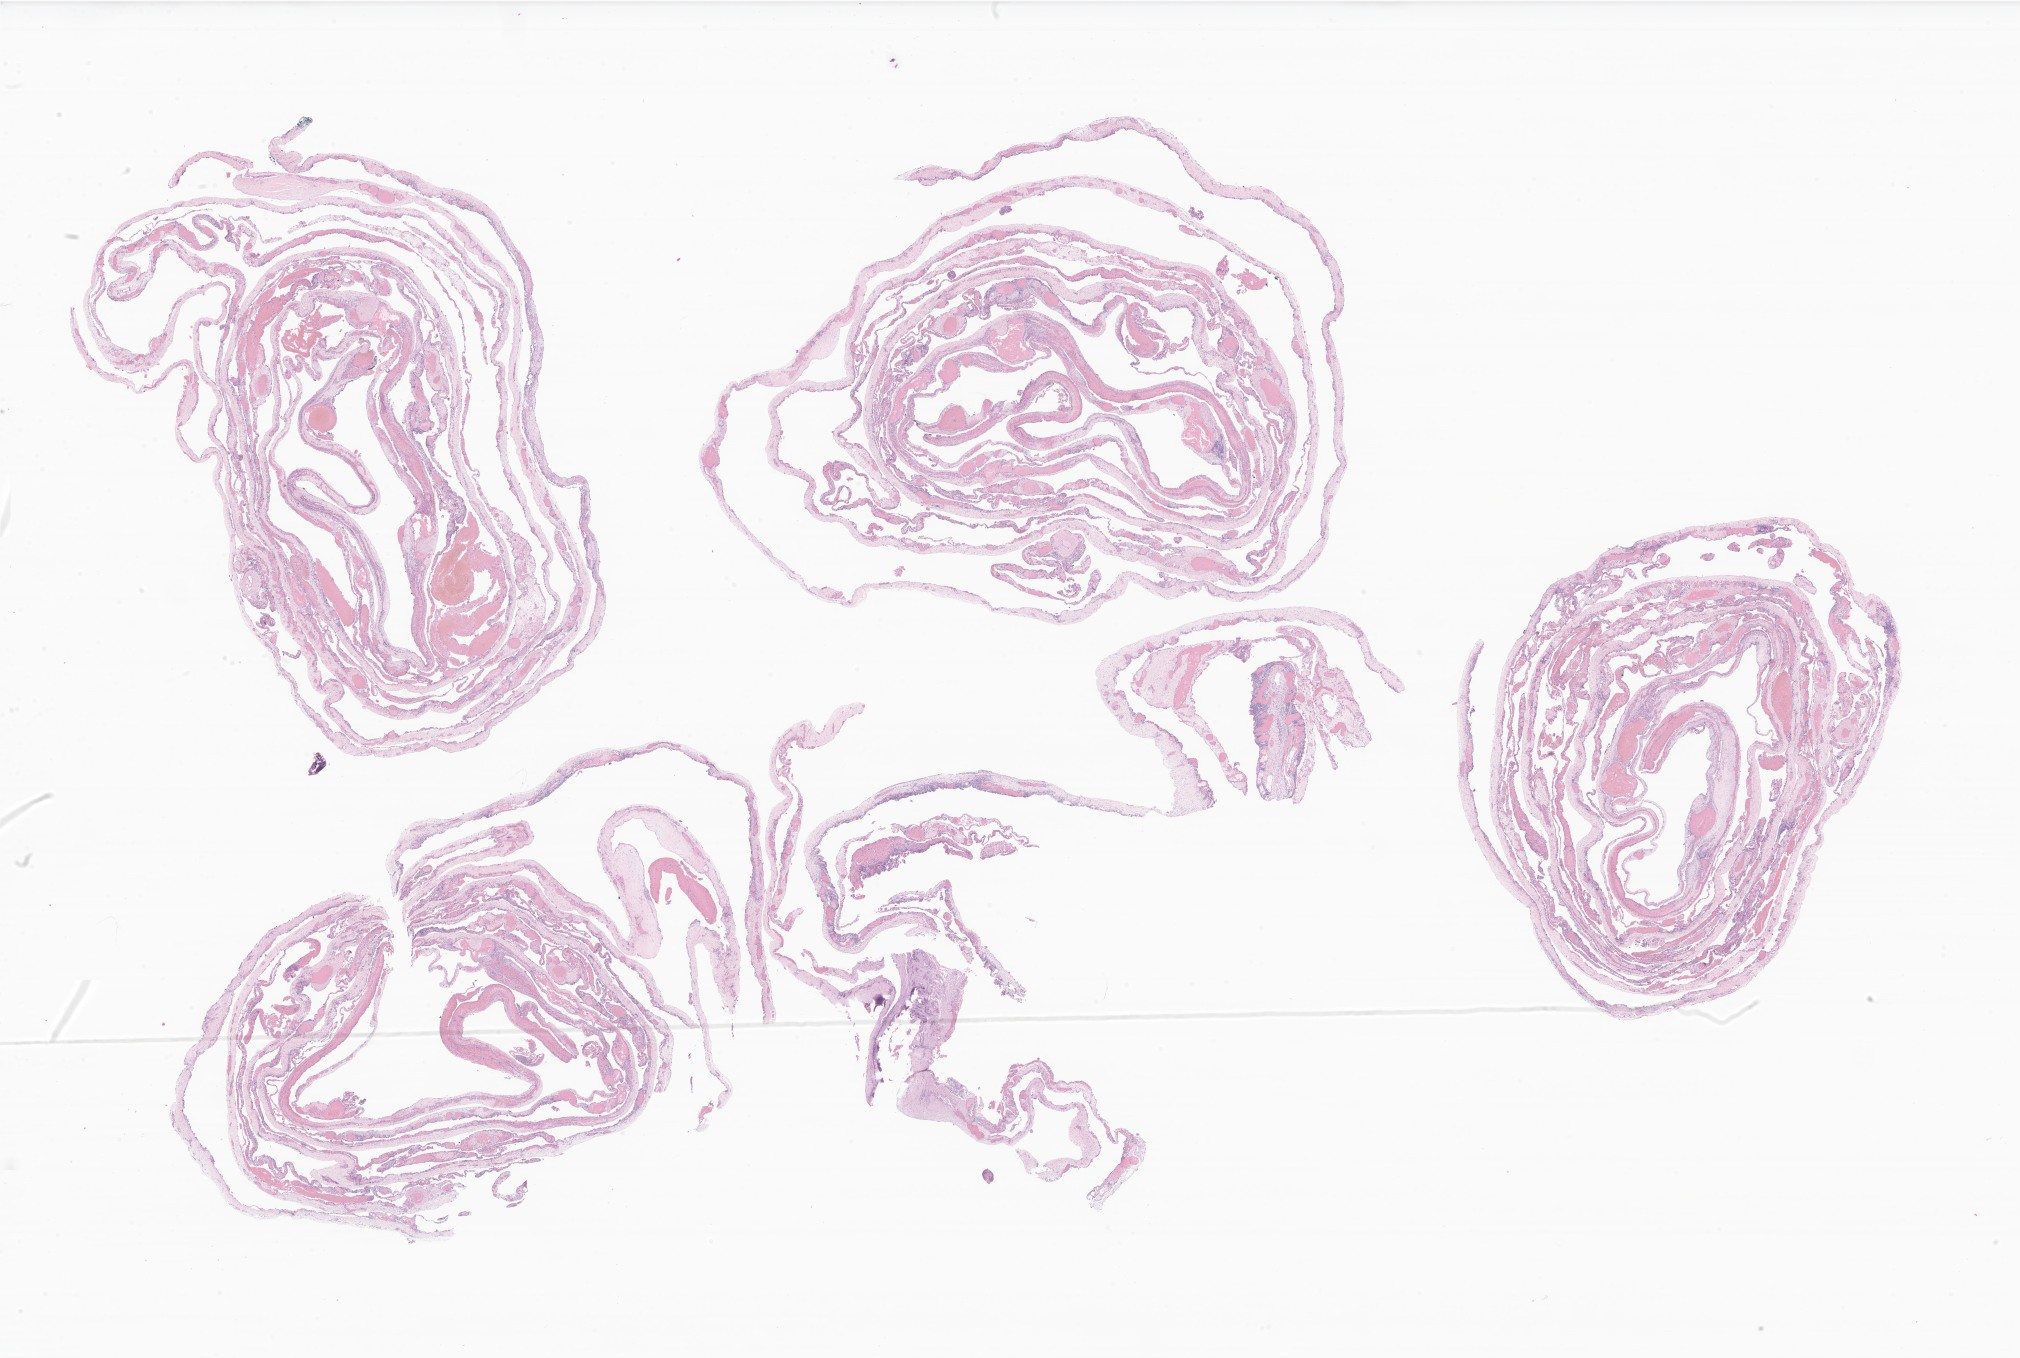
Digitized H&E-stained section of tumor tissue from the lung, low-resolution overview of the scanned area, about 34.1 x 22.9 mm, formalin-fixed paraffin-embedded section. Patient male; age 75 months (6 years 3 months).
• diagnosis (ICD-O-3 morphology term): Pleuropulmonary blastoma